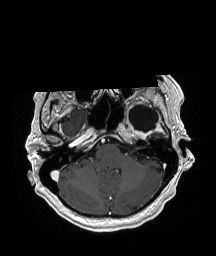
Brain MRI from a brain-tumour surgery series, one axial slice; slice 146 of 192 in the series (ordered by position); T1-weighted post-contrast; 216 × 256 image matrix, field of view 211 × 250 mm. Case-level facts recorded for this patient, not image findings: histopathology: Glioblastoma; WHO grade: 4; IDH mutation: no; tumour location: Left Temporal.
Annotated regions visible in this slice (expert manual segmentation):
- previous resection cavity: bounding box (x1, y1, x2, y2) in pixels: (128, 105, 158, 132)